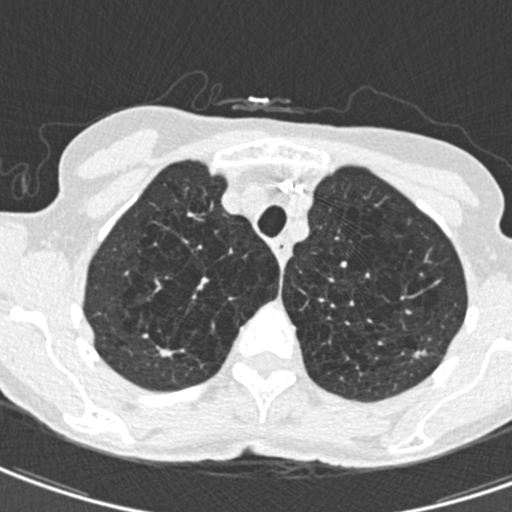
Low-dose screening chest CT, axial slice, second screening round (one year after baseline), lung window (W 1500 / L -600 HU), standard (soft-tissue) reconstruction kernel (B30f), slice 105 of 498 in the series, 512 × 512 image matrix. Female participant, aged 71 years at enrolment.
Expert-annotated lung lesion, bounding box [x1, y1, x2, y2] px = [405, 332, 444, 370]. The screening reader recorded 2 non-calcified nodules or masses ≥4 mm on this exam (right upper lobe, left upper lobe); which of them this box marks is not recorded. Official screen result: positive, change unspecified: nodule(s) >= 4 mm or enlarging nodule(s), mass(es), or other non-specific abnormalities suspicious for lung cancer. Lung cancer was diagnosed 604 days after this screen (after the third annual screen): adenocarcinoma, NOS, left upper lobe, moderately differentiated (G2), stage IA (AJCC 6th edition), 12 mm at pathology.